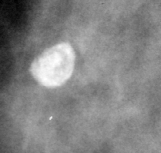
Crop from a digitized film mammogram around one marked abnormality; right breast; MLO view; BI-RADS breast density category 3 (scale 1–4).
Finding: calcifications, morphology round and regular / eggshell; BI-RADS assessment category 2; benign without callback (not worked up further).